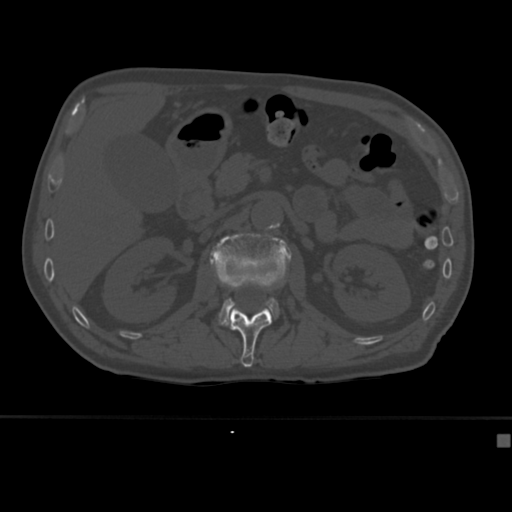
CT including the spine, one axial slice. Position 161 of 430 along the scan axis. Reconstruction kernel Br40s. 120 kVp. Bone window (W 1800 / L 400 HU). 1.5 mm slice thickness. 512 × 512 image matrix, field of view 337 × 337 mm. Patient: male, 64 years. Case-level facts recorded for this patient, not image findings: primary cancer: uterus.
Outlined on this slice (semi-automatically segmented with operator editing):
- L1 vertebra: bounding box (x1, y1, x2, y2) in pixels: (227, 284, 272, 367)
- L2 vertebra: (210, 233, 292, 326)